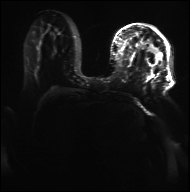
Breast MRI, one axial slice. Diffusion-weighted series; image 2 of 4 stored at this slice position (different b-values; order by instance number). 3 T. 190 × 192 image matrix, field of view 317 × 320 mm. Female patient.
Outlined on this slice (manually delineated by an expert):
- tumour on diffusion-weighted imaging: bounding box <32,45,63,63> (left, top, right, bottom; pixels)